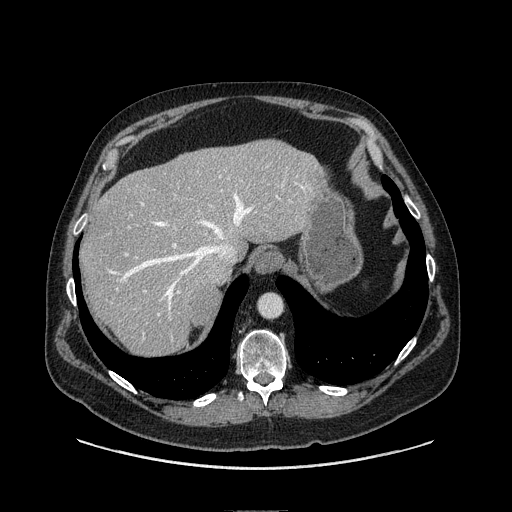
Contrast-enhanced abdominal CT, one axial slice. Position 93 of 149 along the scan axis. Soft-tissue window (W 400 / L 40 HU). 512 × 512 image matrix, field of view 440 × 440 mm. Male patient. From the clinical record (not read from this slice): diagnosis: adrenocortical carcinoma; tumour side: right adrenal; tumour size at pathology: 7.5 cm; Ki-67 index: 15 %.
Structures marked on this image (semi-automatically segmented with operator editing):
- mass: box from (x=193, y=287) to (x=218, y=324) px